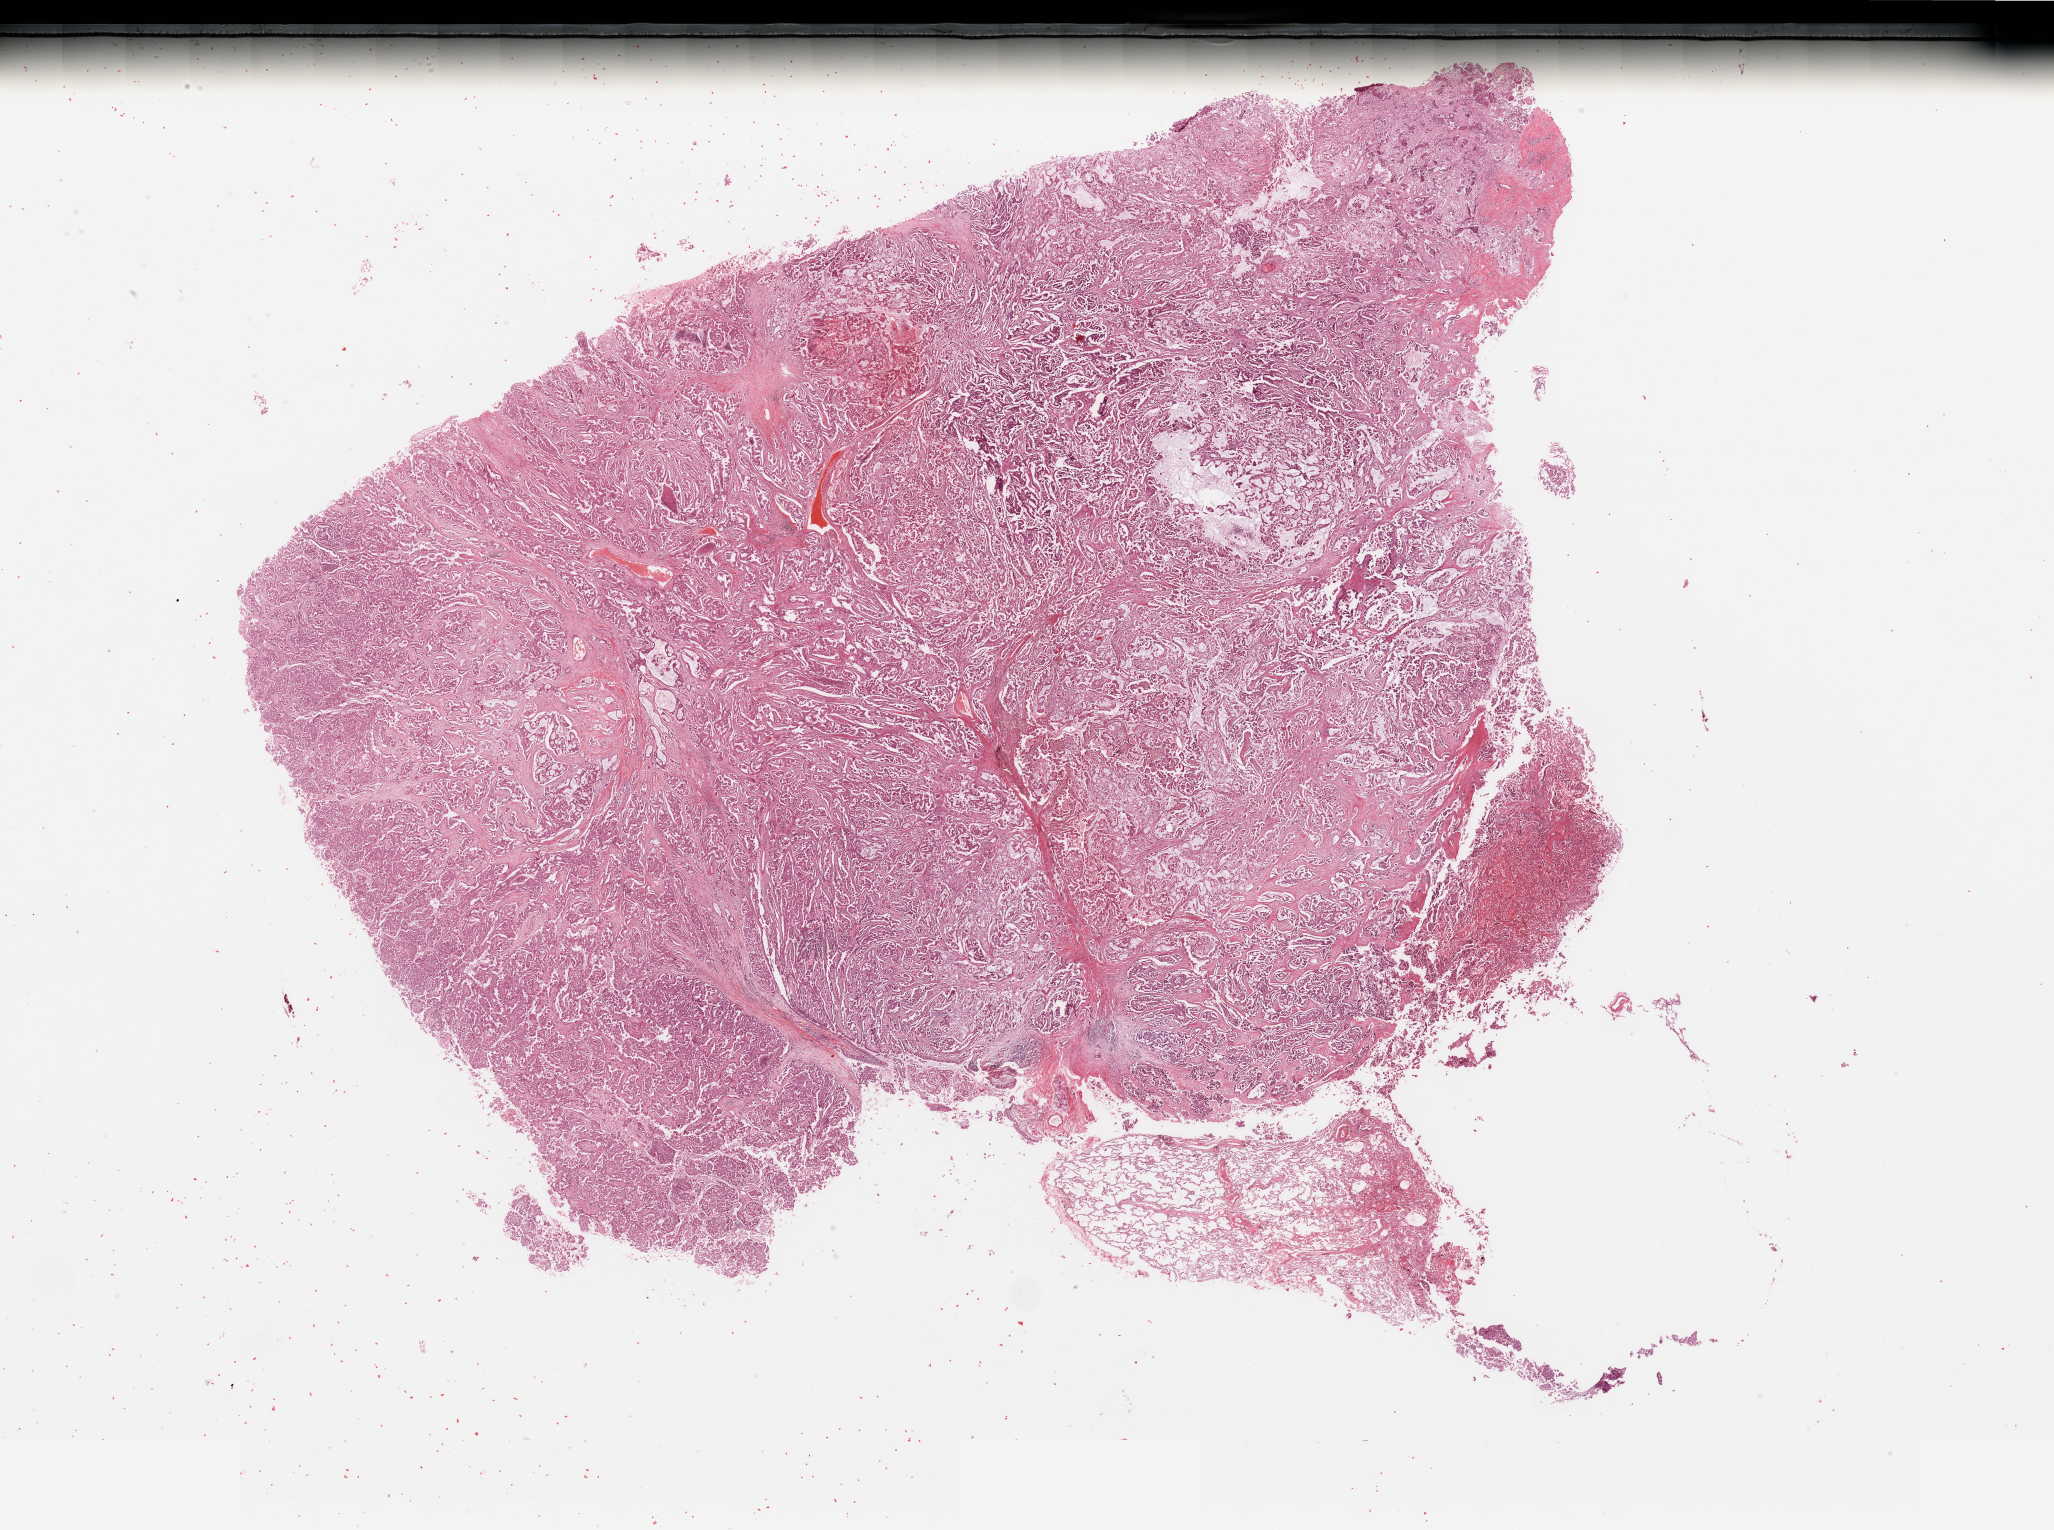
H&E whole-slide image — low-resolution overview of the scanned area, about 32.5 x 24.2 mm; tumour tissue sample, sampled site: lung. Patient: male, age 55 years. Histologic grade: G2 (moderately differentiated). Composition of this section per pathologist review: tumour nuclei 85%, necrosis 2%.
- AJCC pathologic stage: IIIA
- diagnosis: Adenocarcinoma, NOS